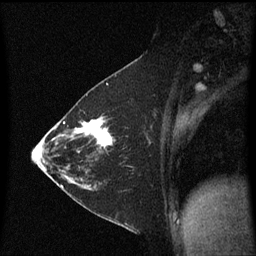
Breast MRI (dynamic contrast-enhanced), one sagittal slice. Position 33 of 60 along the scan axis. Dynamic contrast-enhanced series, image 2 of 3 at this slice position (ordered by acquisition). 1.5 T. TE 4.2 ms, TR 8.4 ms. 2 mm slice thickness. 256 × 256 image matrix, field of view 200 × 200 mm. Female patient, age 36 years. From the clinical record (not read from this slice): setting: breast cancer imaged before/during neoadjuvant chemotherapy; receptor status: HR-positive, HER2-negative.
Structures marked on this image (semi-automatically segmented with operator editing):
- analysis volume of interest (the breast-tissue region the enhancement analysis was run in; not a lesion): bounding box (x1, y1, x2, y2) in pixels: (72, 116, 123, 187)
- tumour enhancement mask (voxels above the 70 % enhancement threshold inside the analysis volume of interest): (72, 118, 115, 187)